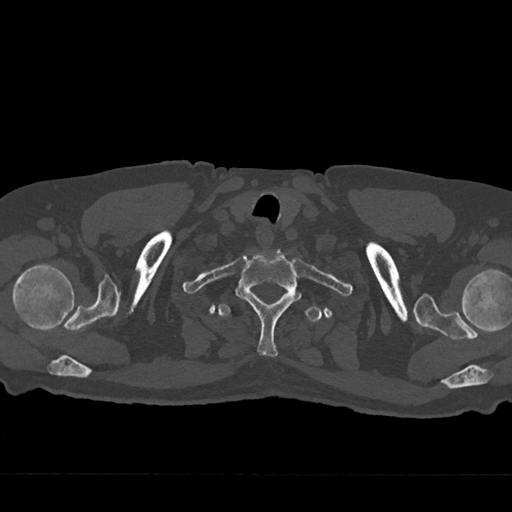
CT including the spine, one axial slice; position 653 of 797 along the scan axis; reconstruction kernel Br40s/3; 120 kVp; bone window (W 1800 / L 400 HU); 512 × 512 image matrix, field of view 377 × 377 mm. Male patient, age 75 years. Case-level facts recorded for this patient, not image findings: primary cancer: renal; vertebrae with lytic lesions (as recorded): T4.
Outlined on this slice (semi-automatic segmentation, software-assisted and operator-edited):
- T1 vertebra: bounding box [x1, y1, x2, y2] px = [235, 250, 299, 357]
- T2 vertebra: [218, 291, 322, 322]